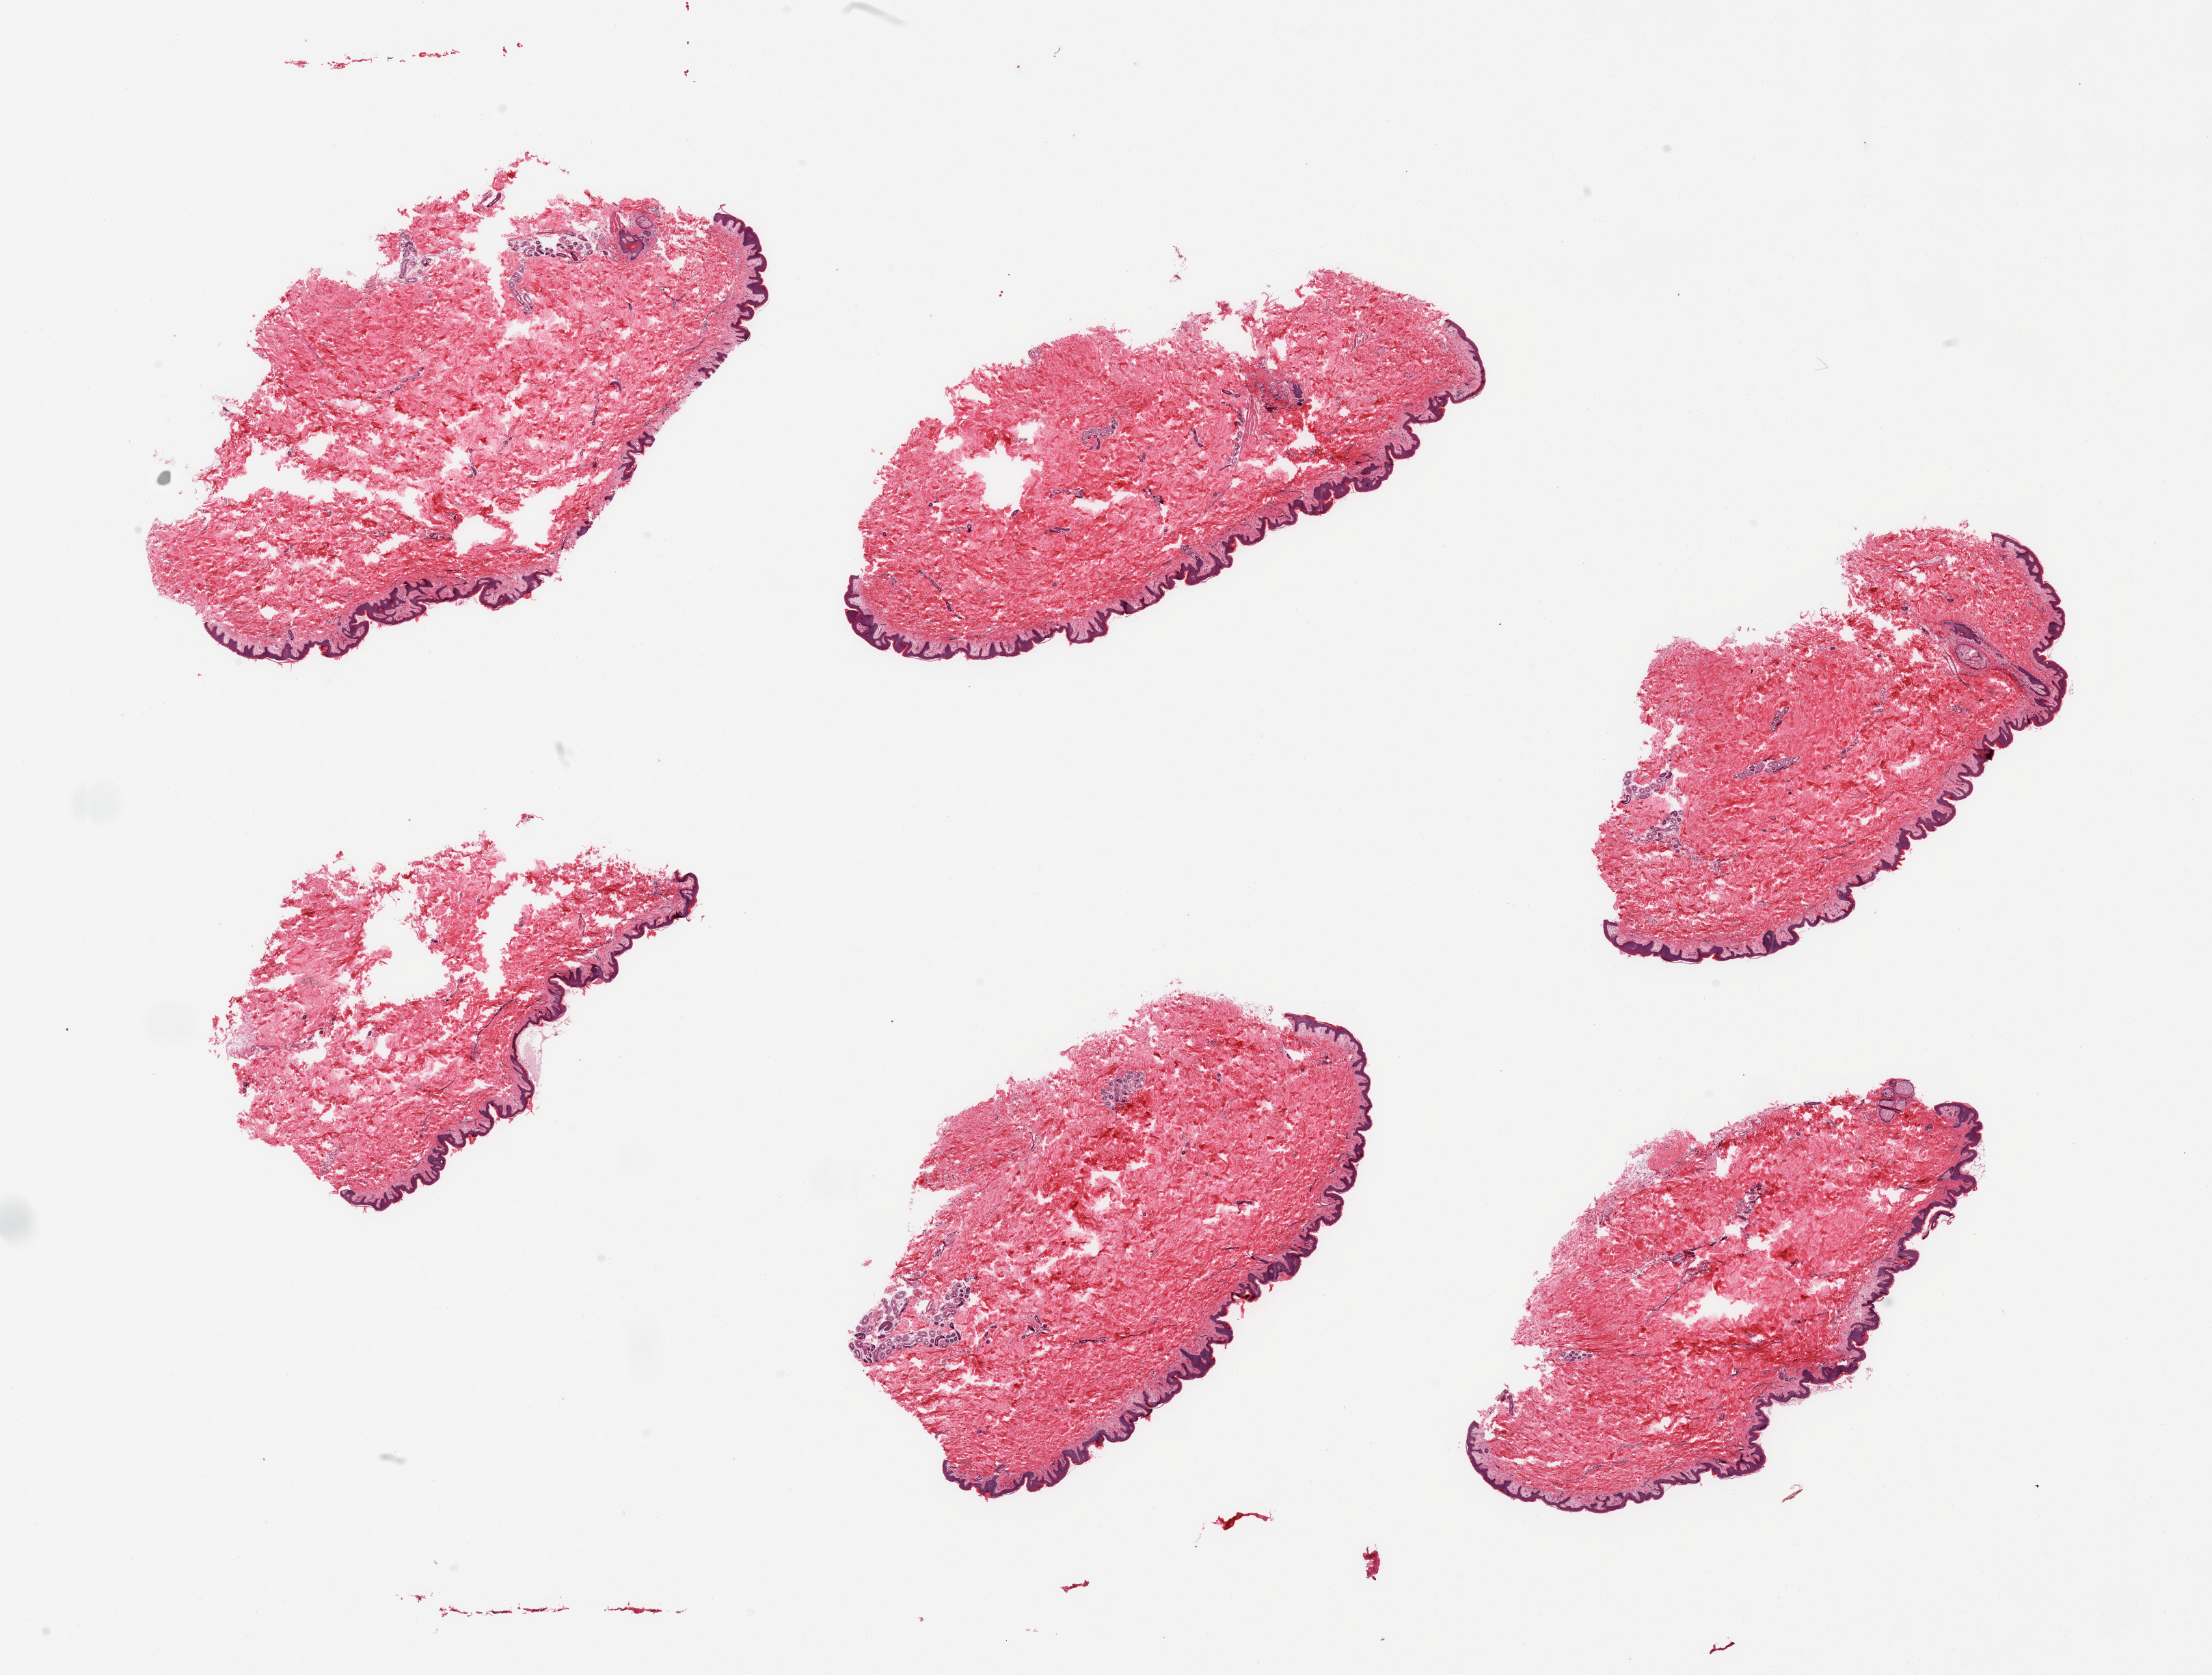
Whole-slide image, haematoxylin and eosin stain, a low-resolution overview of the entire scanned area, about 25.6 x 19.4 mm. PAXgene-fixed paraffin-embedded (PFPE) section. Sampled site (target tissue): skin of suprapubic region. Donor tissue sample.
Review note (as recorded): 6 pieces; well trimmed.